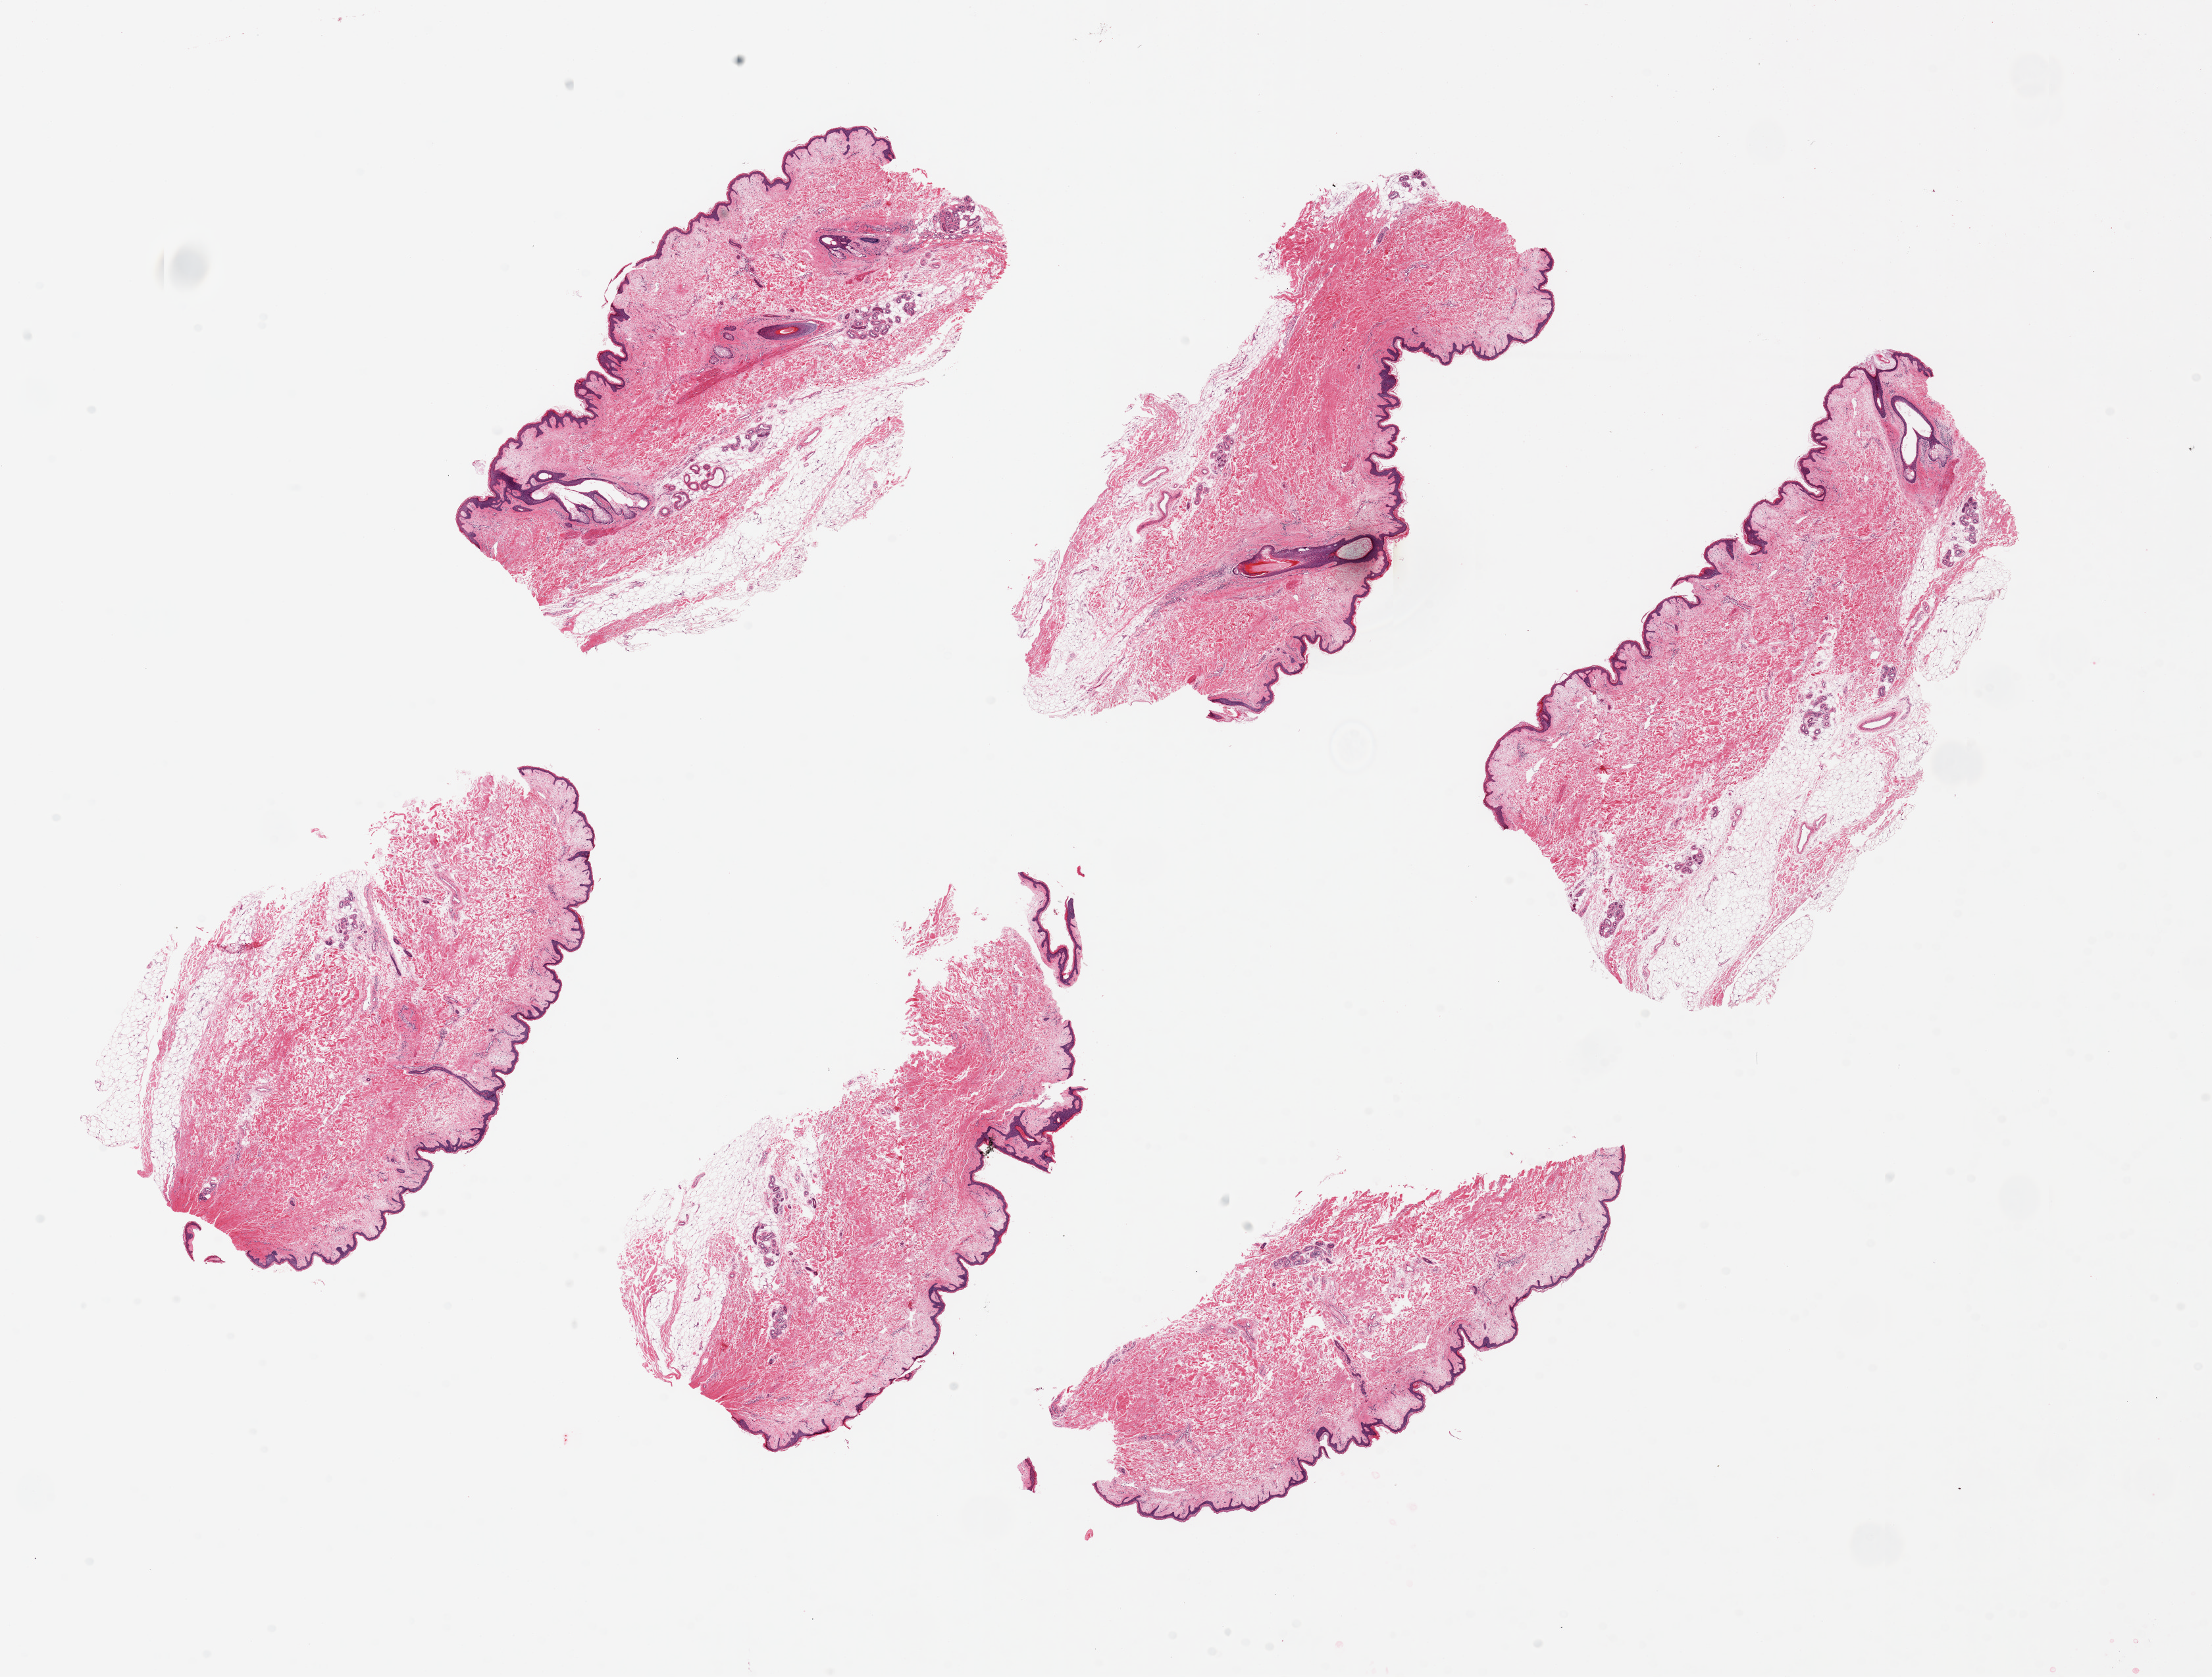
H&E whole-slide image — shown as a low-resolution overview of the whole scanned area (about 26.6 x 20.2 mm, acquisition: 20x scan); PAXgene-fixed paraffin-embedded (PFPE) section; sampled site (target tissue): skin of suprapubic region; donor tissue sample. Male donor.
Pathologist's review note for this sample: 6 pieces, up to 8x3mm; 3 have up to 1.5mm subcutaneous adipose tissue.